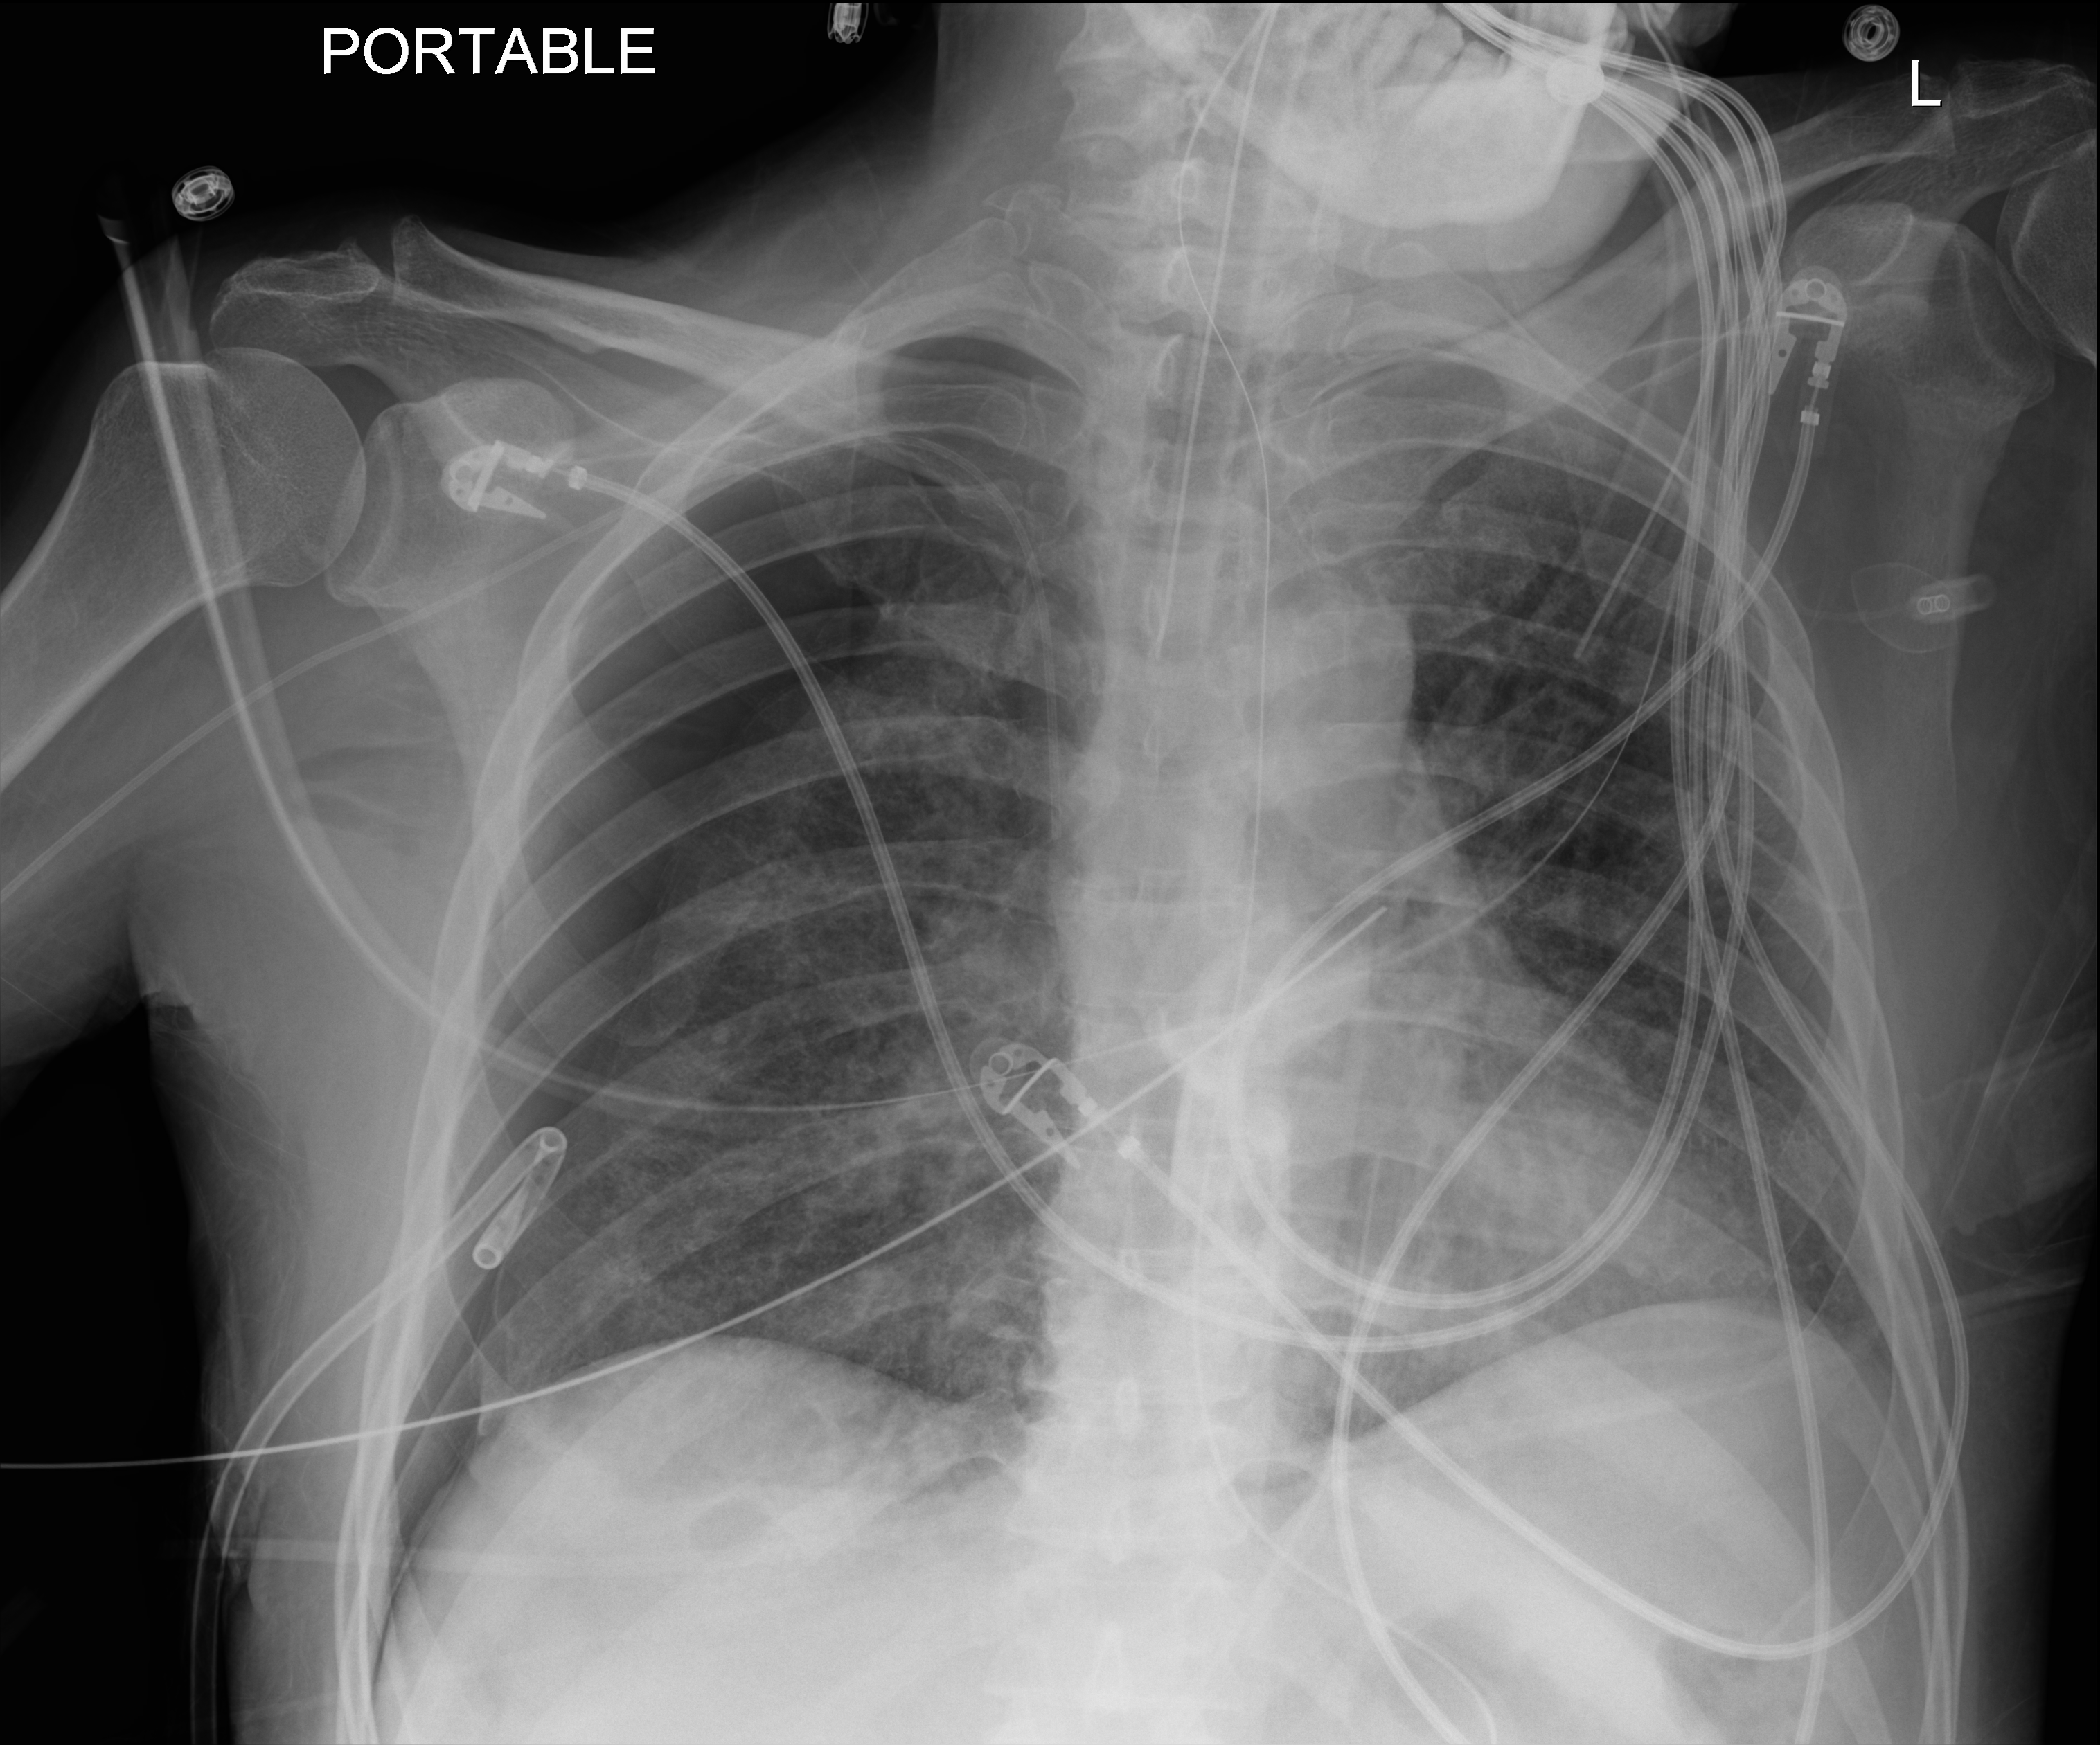
Chest X-ray (portable); anteroposterior (AP) projection. Male patient hospitalised with COVID-19, age 18–59 years.
Hospital-stay facts (about this admission, not read from this image; timing relative to this image not recorded):
- admitted to intensive care during this hospital stay: yes
- chronic kidney disease (admission record): no
- mechanically ventilated during this hospital stay: yes